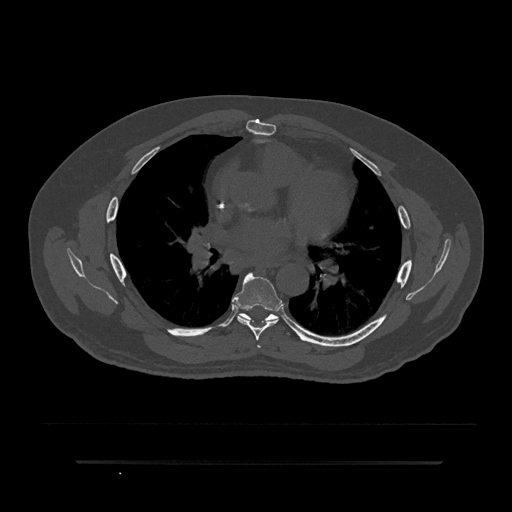
CT including the spine, one axial slice. Position 511 of 797 along the scan axis. Reconstruction kernel Br40s/3. Bone window (W 1800 / L 400 HU). 512 × 512 image matrix, field of view 464 × 464 mm. Male patient, age 59 years. Case-level facts recorded for this patient, not image findings: primary cancer: bile ducts.
Structures marked on this image (semi-automatically segmented with operator editing):
- T5 vertebra: bounding box <257,345,261,348> (left, top, right, bottom; pixels)
- T6 vertebra: <232,272,282,341>
- T7 vertebra: <240,313,290,335>